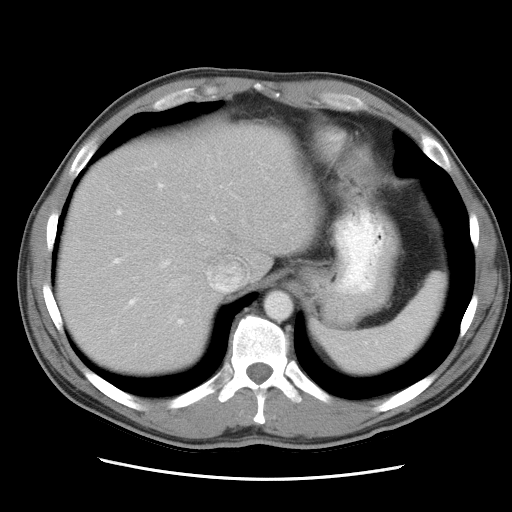
Contrast-enhanced abdominal CT, one axial slice; position 24 of 34 along the scan axis; 120 kVp; intravenous contrast given; soft-tissue window (W 400 / L 40 HU); 7.5 mm slice thickness; 512 × 512 image matrix, field of view 360 × 360 mm. Male patient, age 40 years. From the clinical record (not read from this slice): diagnosis: colorectal cancer liver metastases, imaged before liver resection; multiple liver metastases: yes; largest metastasis: 1.5 cm; disease in both lobes: yes.
Structures marked on this image (expert manual segmentation):
- hepatic veins: bounding box <156,266,242,298> (left, top, right, bottom; pixels)
- liver: <60,119,317,372>
- planned liver remnant (the part of the liver to remain after resection): <59,119,317,372>
- portal vein (with intrahepatic branches): <113,184,199,325>